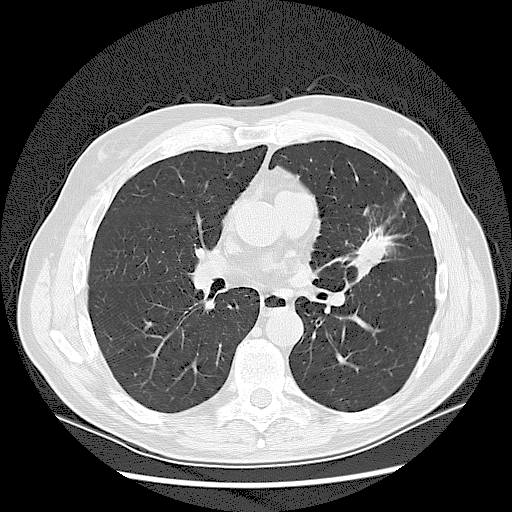
Low-dose screening chest CT, one axial slice; 120 kVp; lung window (W 1500 / L -600 HU); 2.5 mm slice thickness; 512 × 512 image matrix, field of view 380 × 380 mm.
Outlined on this slice (expert manual segmentation):
- lesion 1 (tumor, upper lobe of left lung): bounding box [x1, y1, x2, y2] px = [355, 234, 388, 275]